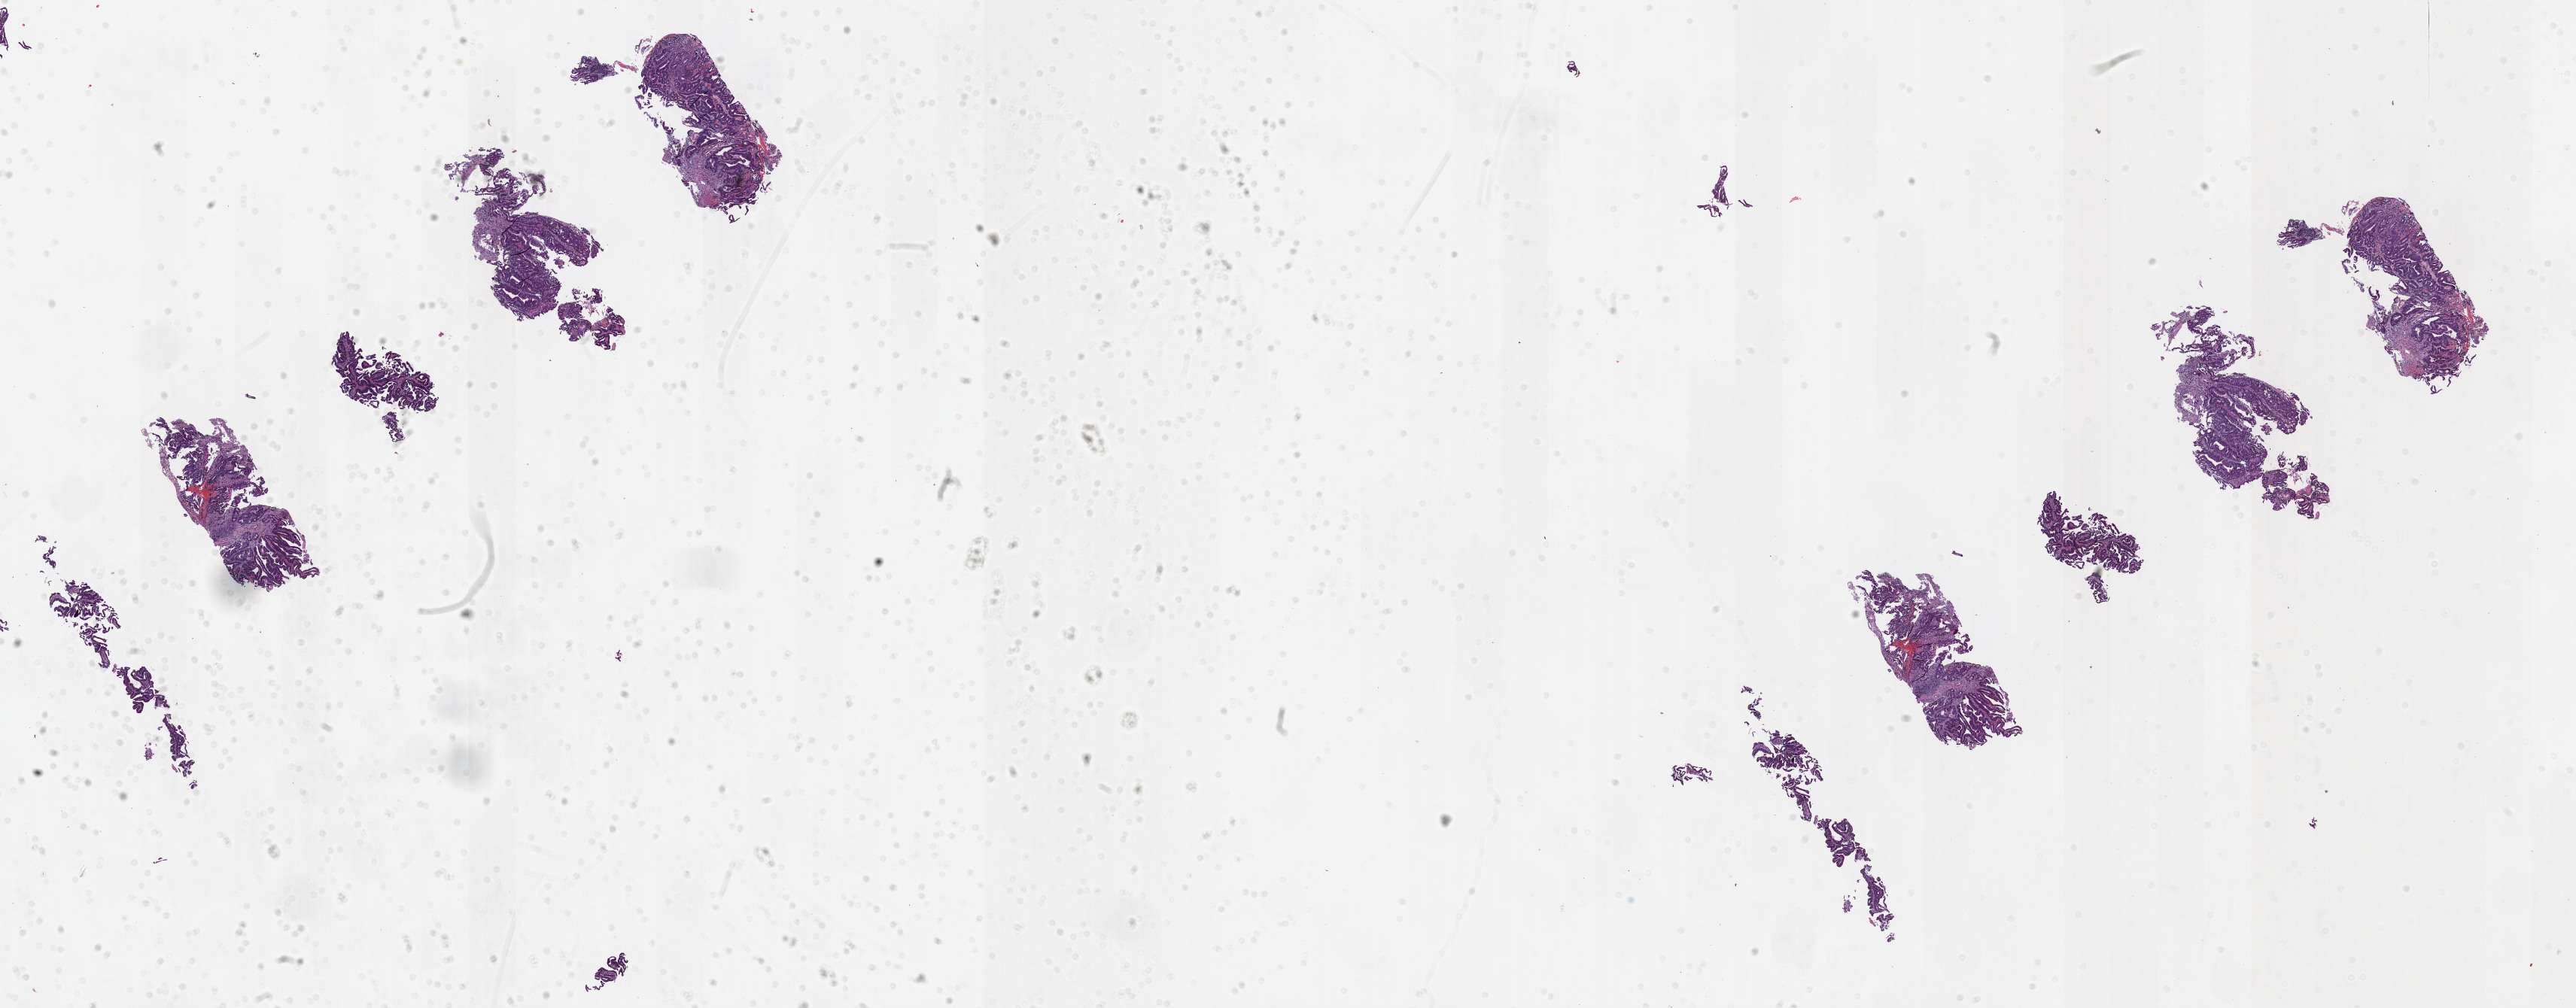
H&E-stained whole-slide image, whole scanned area (about 27.7 x 10.8 mm) shown as a low-resolution overview, formalin-fixed paraffin-embedded (FFPE) diagnostic section, primary tumour sample from the esophagus. Male, age 56 years at initial diagnosis. Histologic grade: G2 (moderately differentiated). Pathologist review of this section (percent, as recorded): tumour cells 80%, tumour nuclei 80%, normal cells 0%, stromal cells 20%, necrosis 0%. Inflammatory infiltration, as recorded: lymphocyte infiltration 40%, monocyte infiltration 20%, neutrophil infiltration 20%.
Histologic diagnosis: Adenocarcinoma, NOS (lower third of esophagus).